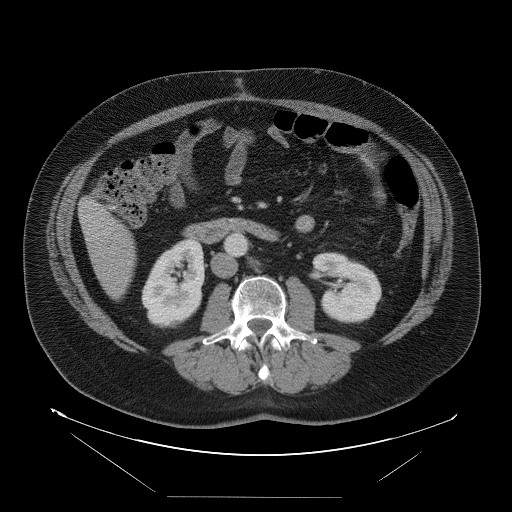
Contrast-enhanced abdominal CT, one axial slice. Position 23 of 114 along the scan axis. Intravenous contrast given. Soft-tissue window (W 400 / L 40 HU). 512 × 512 image matrix, field of view 500 × 500 mm. Male patient, age 61 years. Case-level facts recorded for this patient, not image findings: diagnosis: colorectal cancer liver metastases, imaged before liver resection; multiple liver metastases: no; largest metastasis: 6.5 cm.
Outlined on this slice (outlined manually by an expert reader):
- liver: bounding box (x1, y1, x2, y2) in pixels: (80, 199, 135, 299)